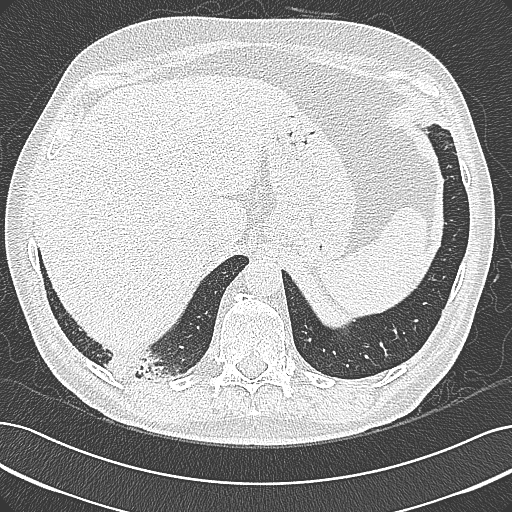
Chest CT (low-dose screening protocol), one axial image, baseline annual screen, lung window (W 1500 / L -600 HU), 1 mm slice thickness, 512 × 512 image matrix. Male, age 68 years at enrolment. Former smoker at enrolment.
• Expert-annotated lung lesion, bounding box (x1, y1, x2, y2) in pixels: (93, 336, 195, 396).
• No non-calcified nodule or mass ≥4 mm was recorded by the screening reader at this exam.
• Official screen result: negative screen, significant abnormalities not suspicious for lung cancer.
• Later outcome: lung cancer diagnosed 154 days after this screen — mucinous adenocarcinoma, right lower lobe, well differentiated (G1), stage IB (AJCC 6th edition), 50 mm at pathology.